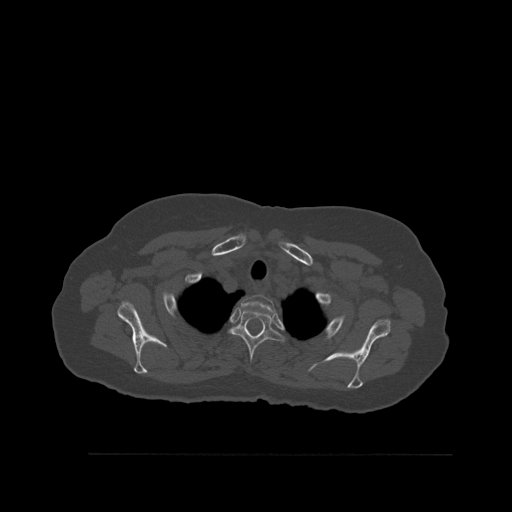
CT including the spine, one axial slice; position 433 of 527 along the scan axis; bone window (W 1800 / L 400 HU); 1.5 mm slice thickness; 512 × 512 image matrix, field of view 470 × 470 mm. Female patient, age 73 years. Case-level facts recorded for this patient, not image findings: primary cancer: breast; vertebrae with lytic lesions (as recorded): L2.
Structures marked on this image (semi-automatically segmented with operator editing):
- T1 vertebra: bounding box [x1, y1, x2, y2] px = [240, 295, 275, 313]
- T2 vertebra: [230, 307, 283, 370]